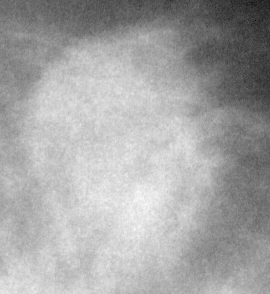
Crop from a digitized film mammogram around one marked abnormality; right breast; CC view.
- Marked abnormality: mass, shape round, margins ill defined; BI-RADS assessment category 4; subtlety rating 4 on a 1 (subtle) to 5 (obvious) scale; pathology (as recorded): malignant.